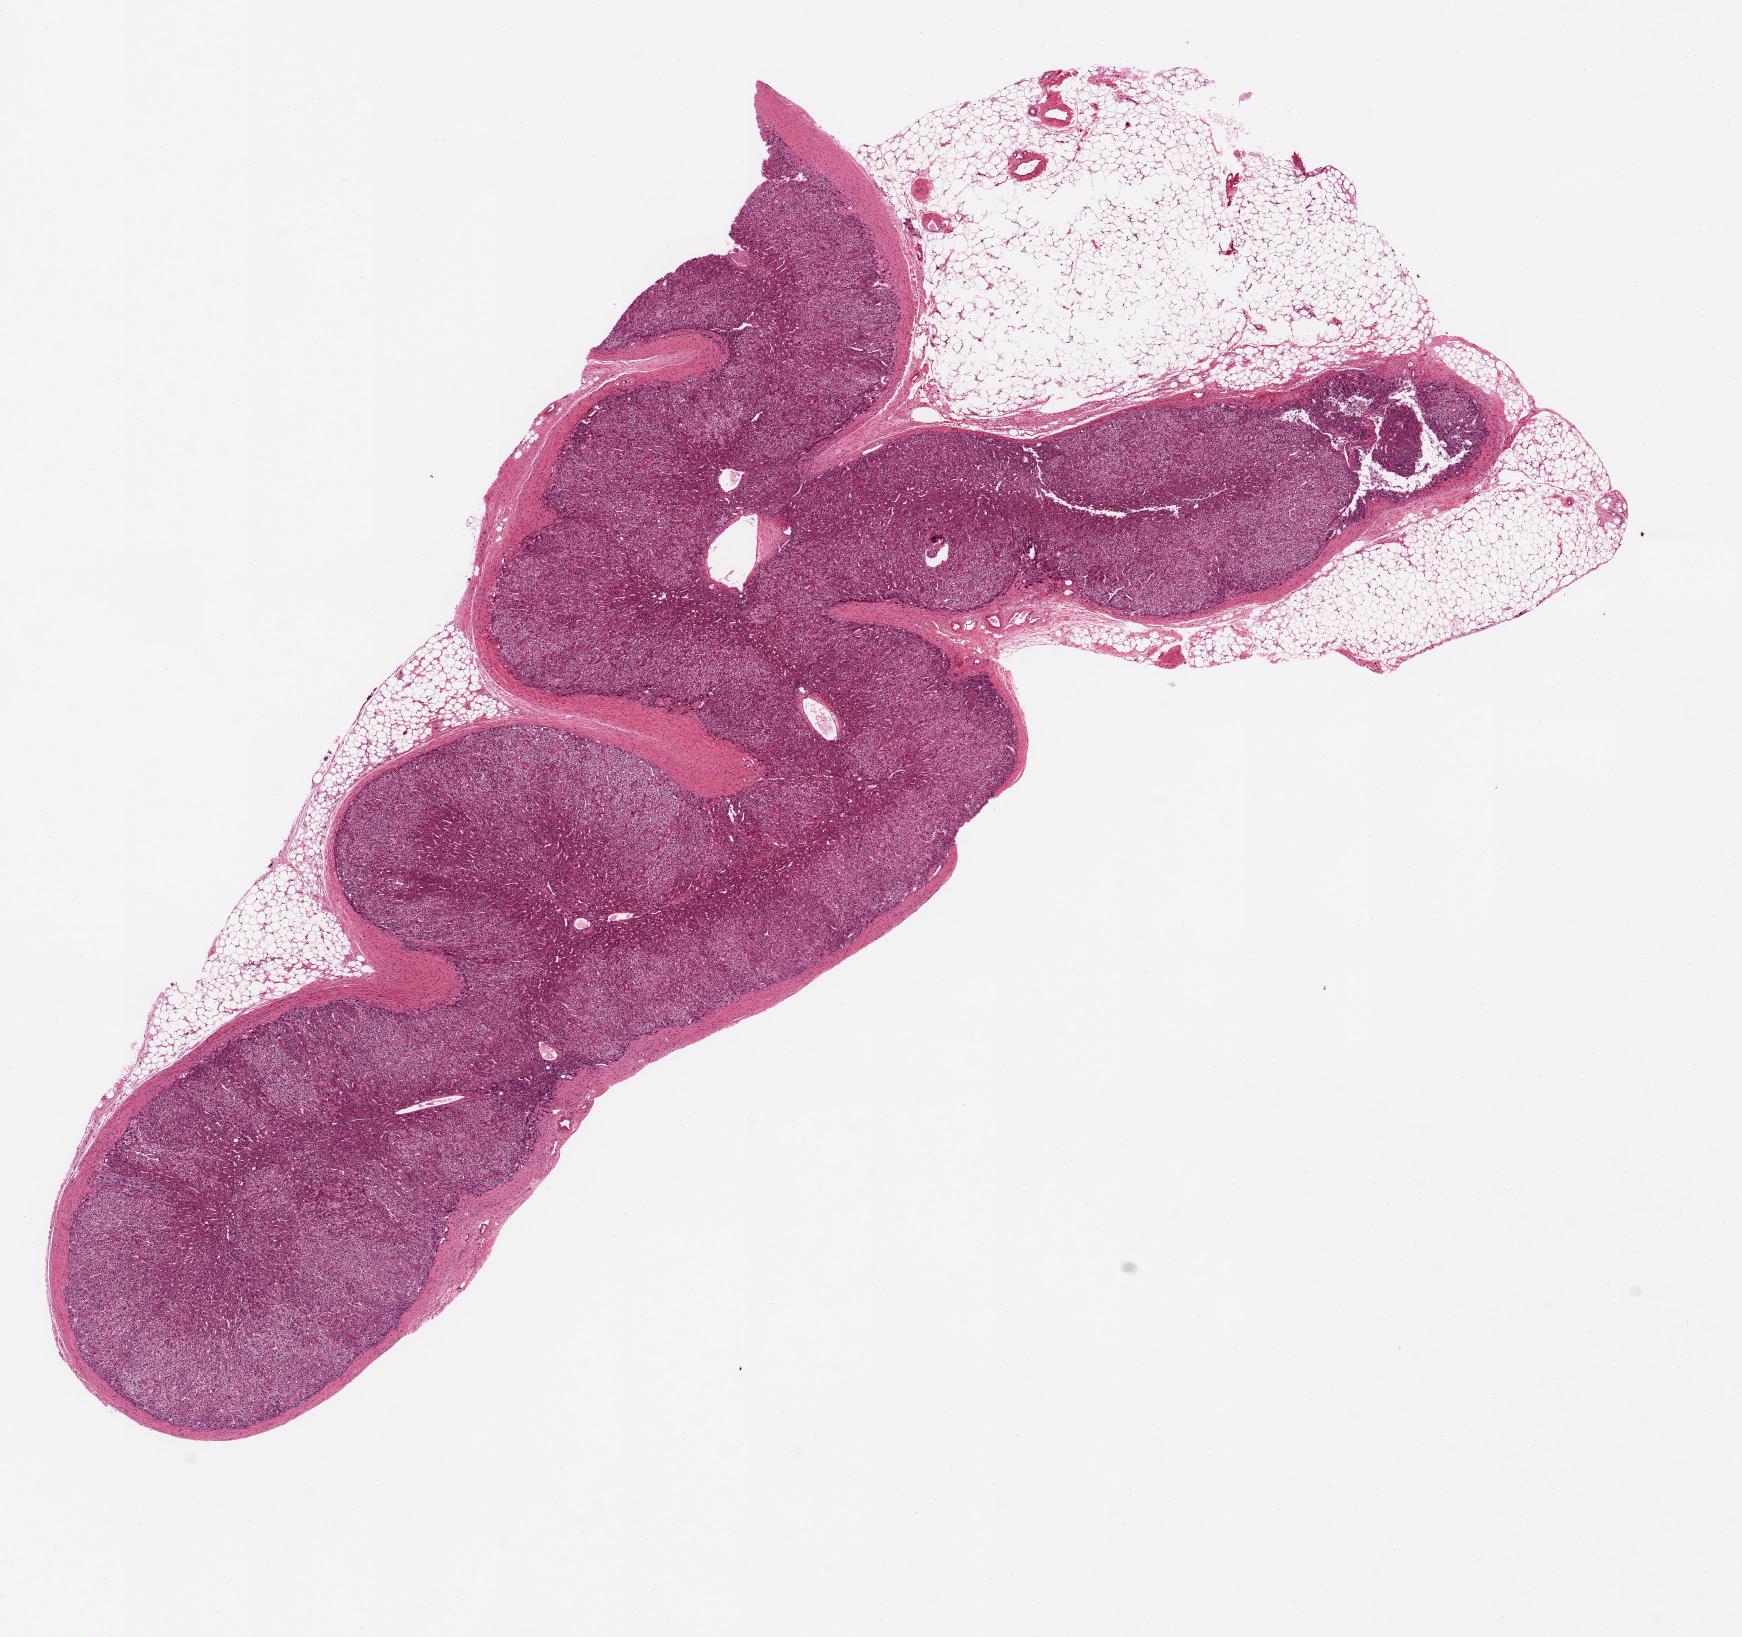
Whole-slide image, haematoxylin and eosin stain, brightfield, low-resolution overview of the scanned area, about 13.8 x 13.0 mm; PAXgene-fixed paraffin-embedded (PFPE) section; target tissue: adrenal gland; donor tissue sample. Donor sex: female.
Review note (as recorded): 1 piece.